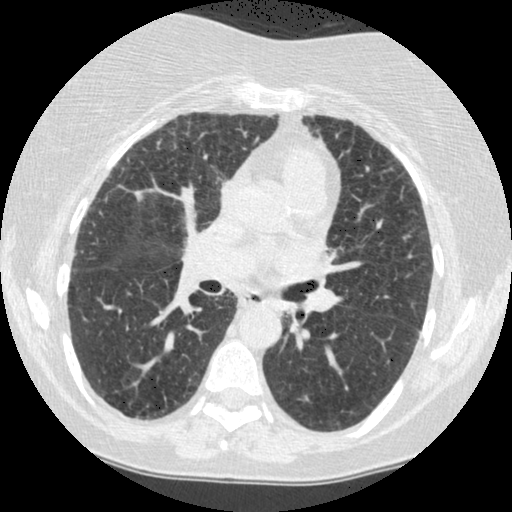
Chest CT (low-dose screening protocol), one axial image; first (baseline) screen; lung window (W 1500 / L -600 HU); standard (soft-tissue) reconstruction kernel (STANDARD); slice 202 of 442 in the series. Female participant, aged 60 years at enrolment.
Expert reader's lesion annotation, bounding box <270,294,310,336> (left, top, right, bottom; pixels). The screening reader recorded 2 non-calcified nodules or masses ≥4 mm on this exam; which of them this box marks is not recorded. Official screen result: positive, change unspecified: nodule(s) >= 4 mm or enlarging nodule(s), mass(es), or other non-specific abnormalities suspicious for lung cancer.